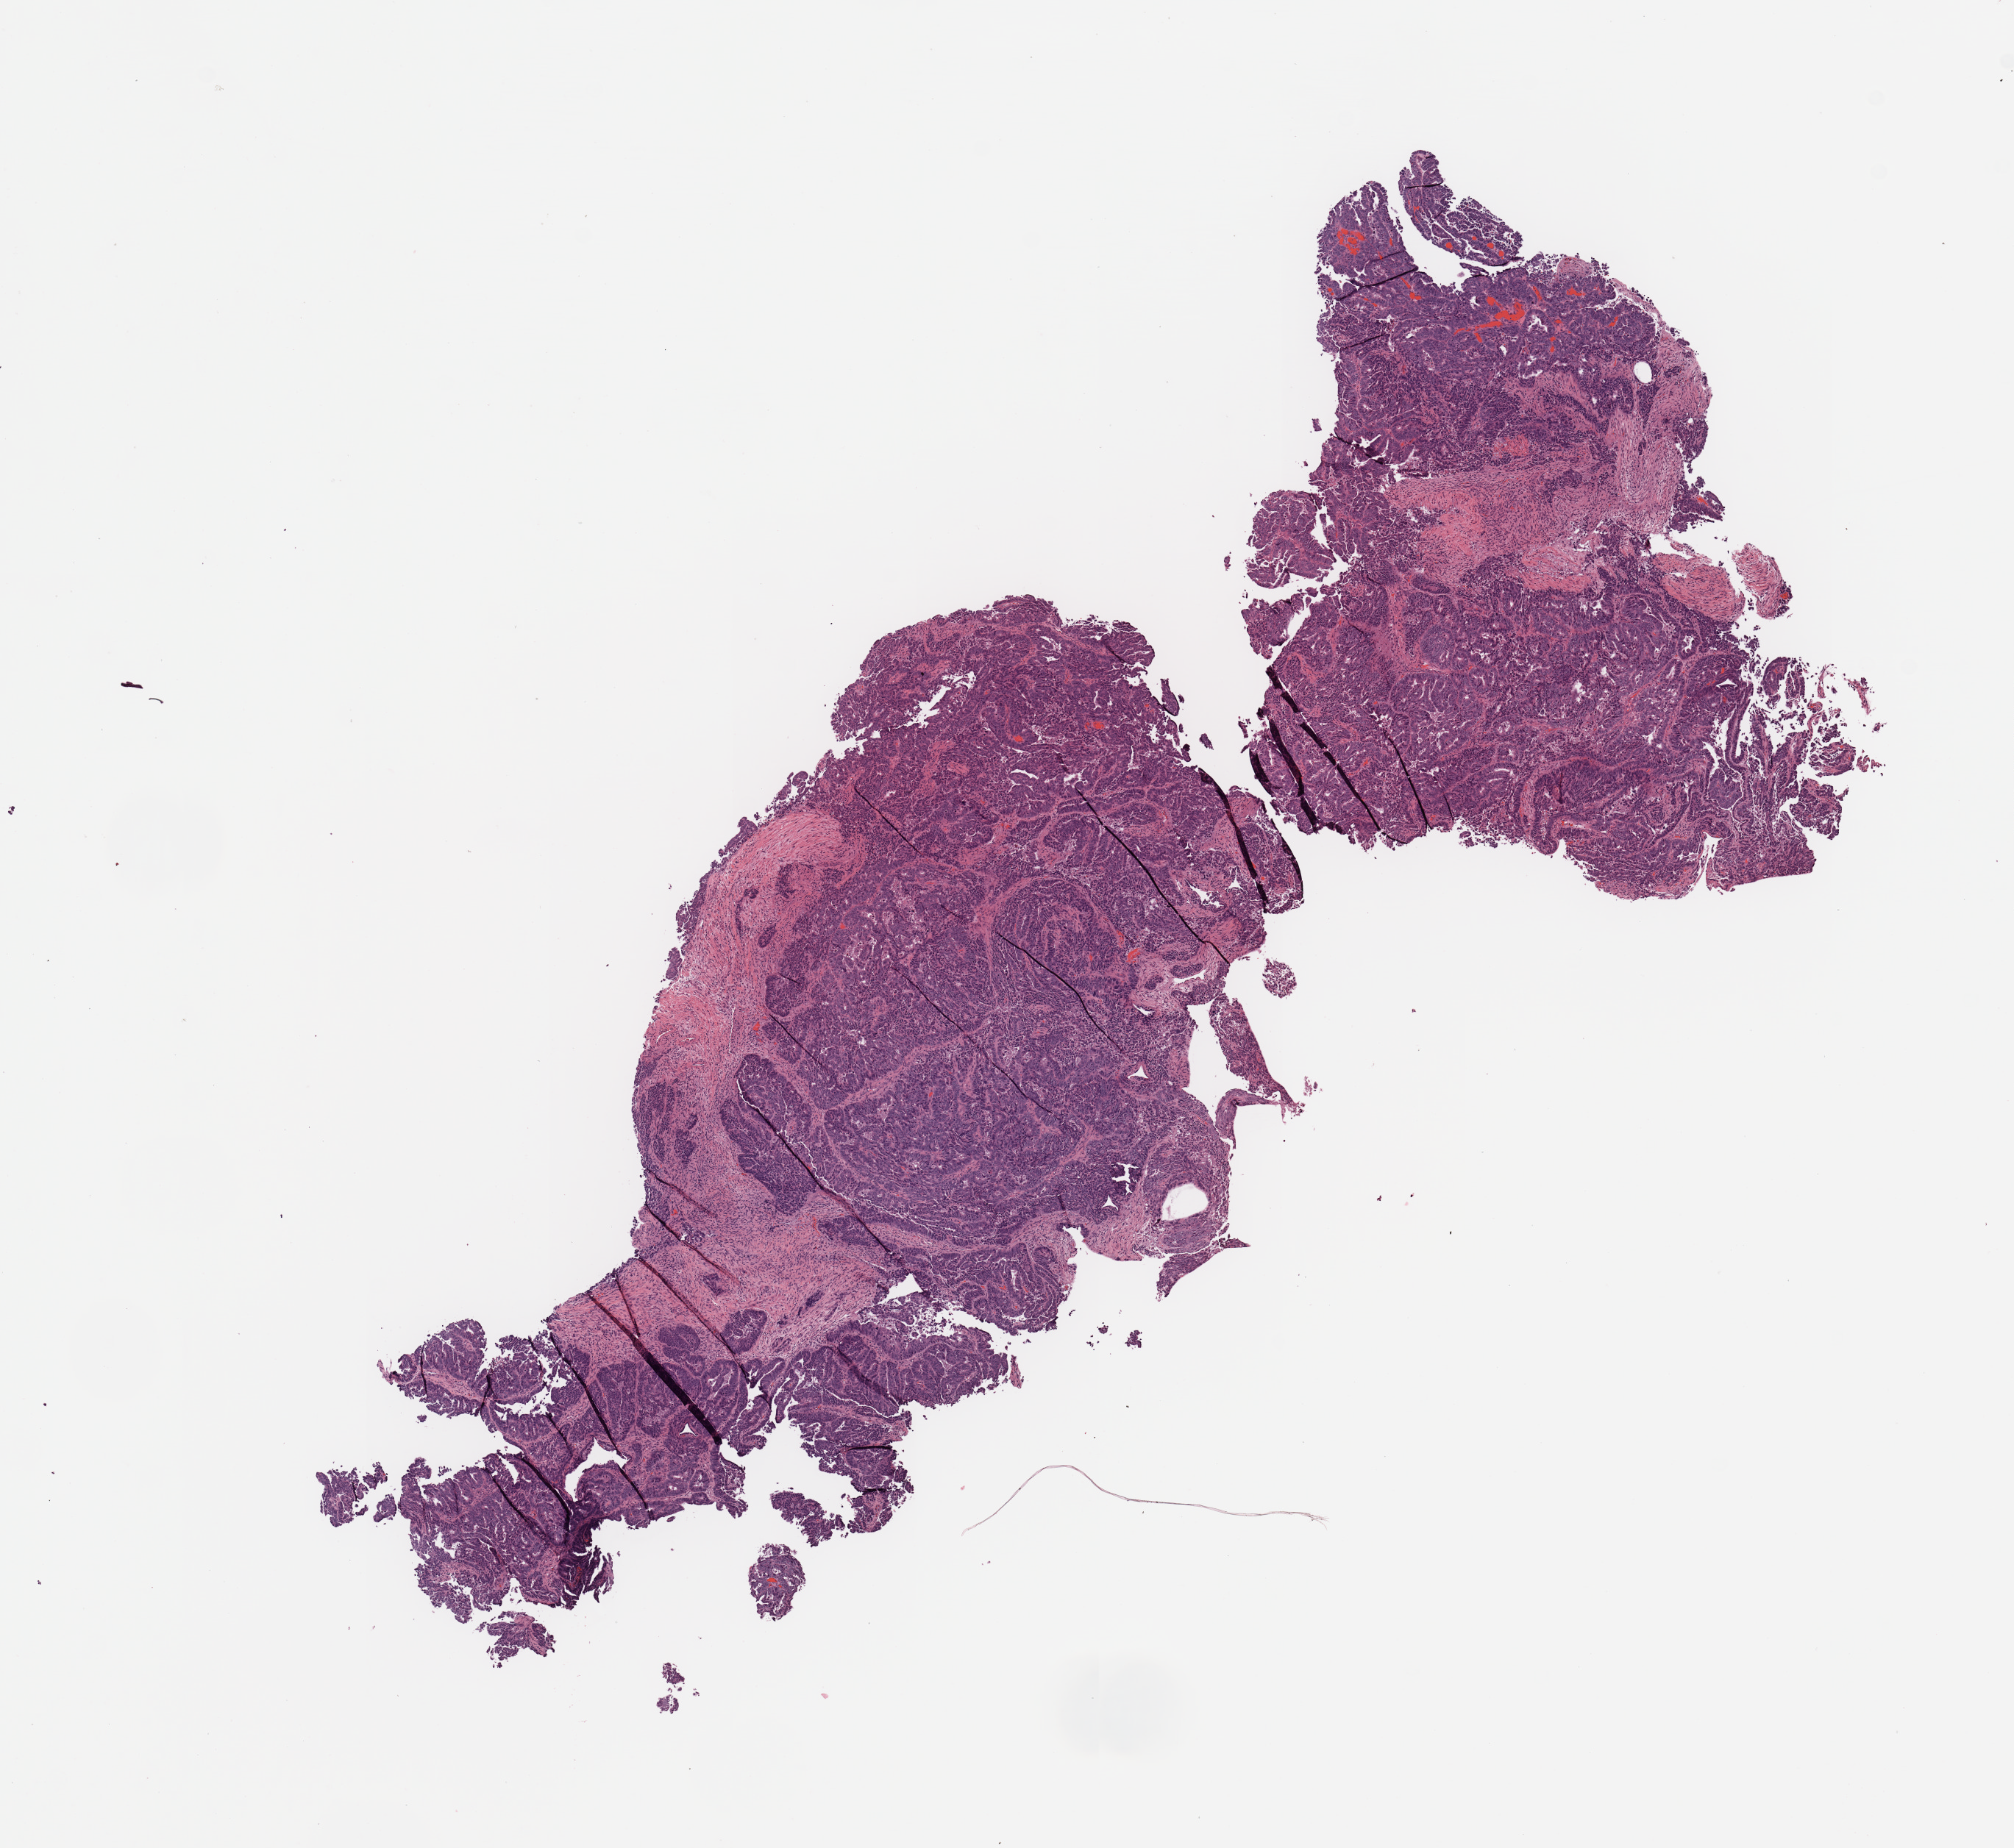
Digitized H&E-stained tissue section (whole slide) — shown as a low-resolution overview of the whole scanned area (about 10.8 x 9.9 mm, acquisition: 20x scan), tumour tissue sample, uterus. Patient: female, age 67 years. Histologic grade: G3 (poorly differentiated).
Histologic diagnosis: Endometrioid adenocarcinoma, NOS. AJCC pathologic stage: IB.